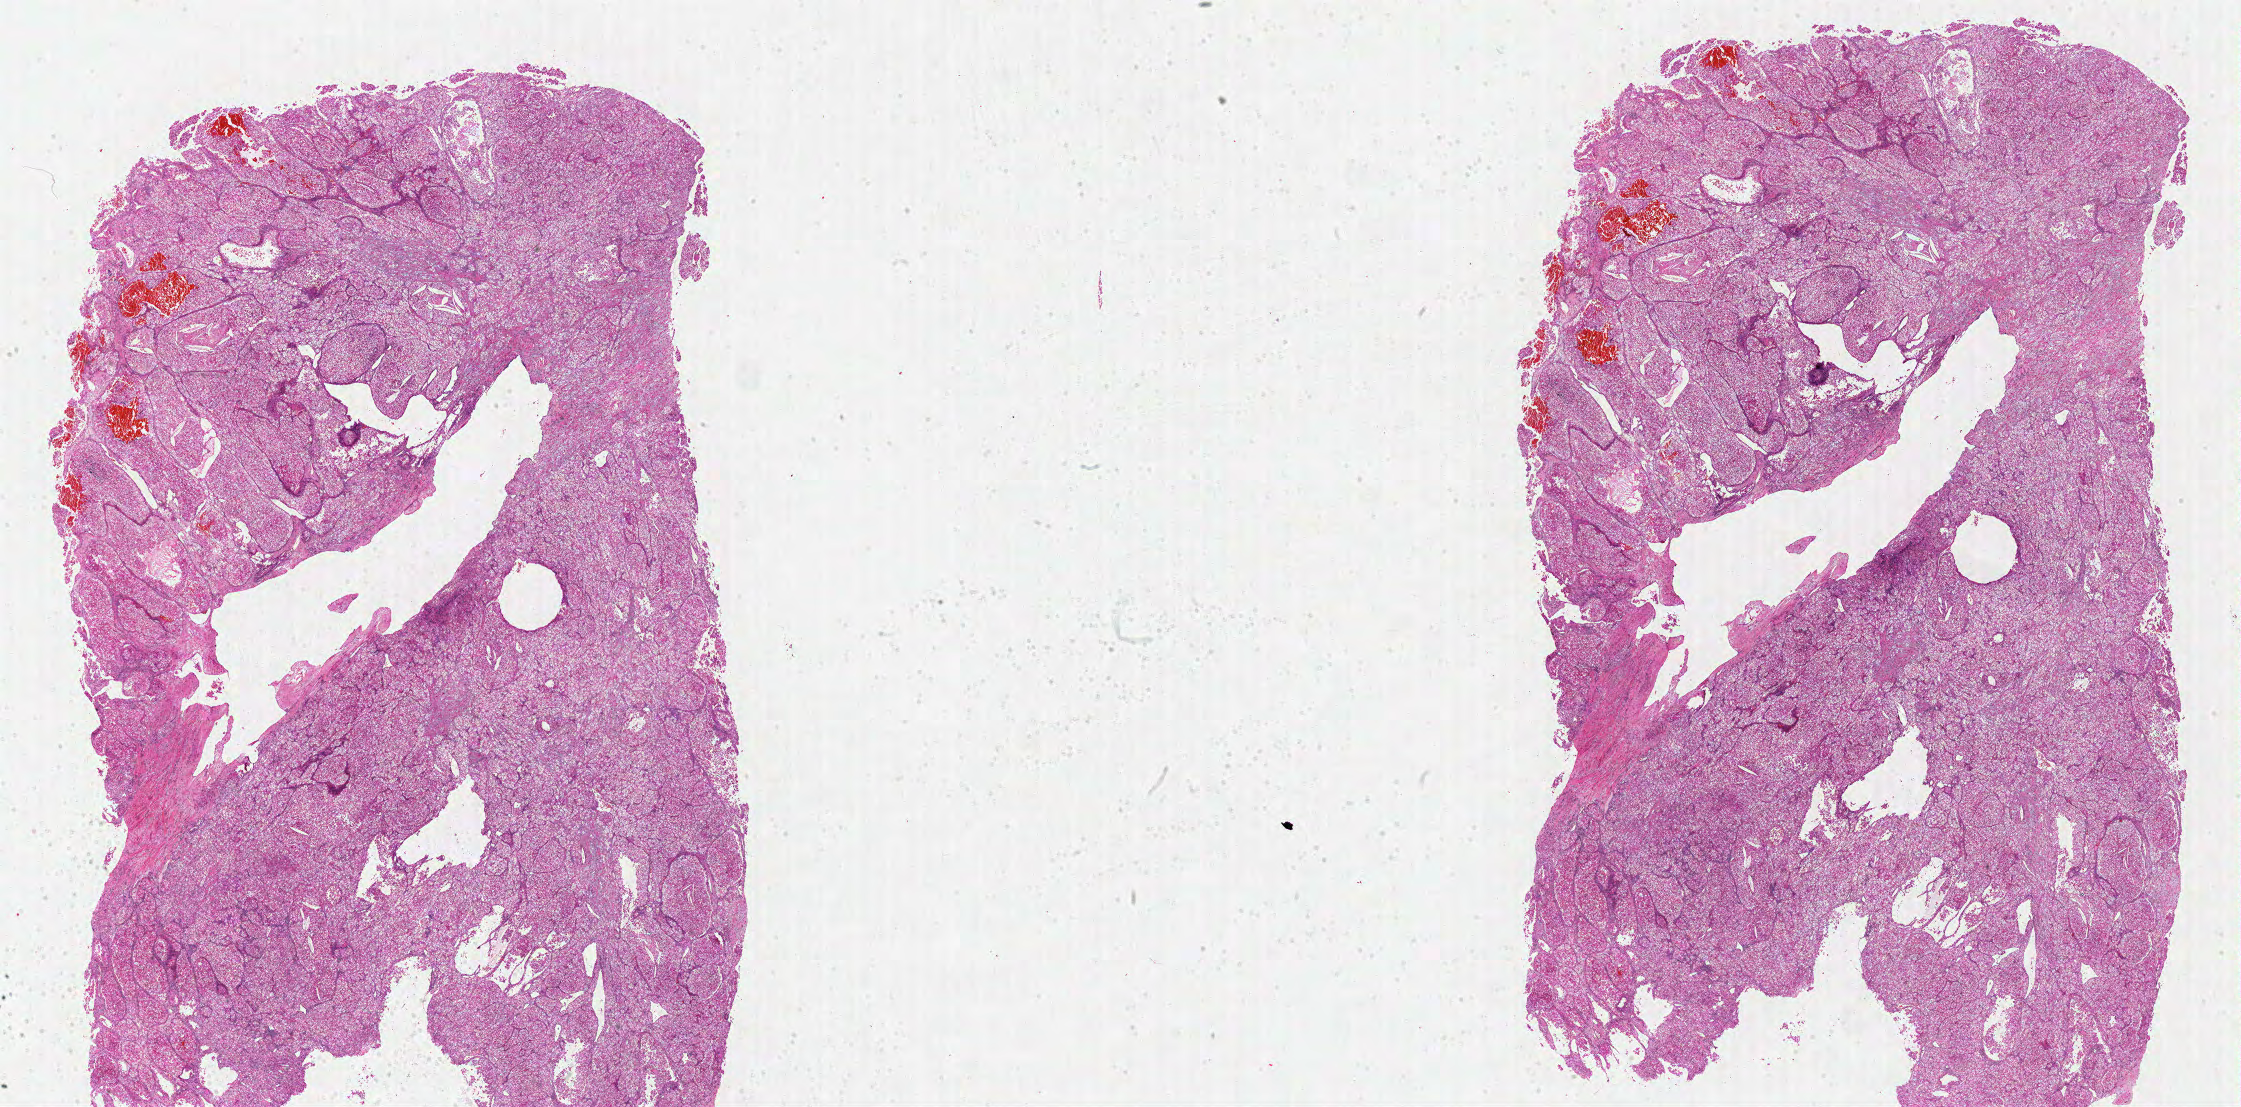
Whole-slide histology image, Hematoxylin and eosin (H&E) stained, a low-resolution overview of the entire scanned area, about 35.2 x 17.4 mm (acquisition: 40x scan). Formalin-fixed paraffin-embedded (FFPE) diagnostic section. Primary tumour sample from the kidney. Male patient; age at initial diagnosis 71 years. Histologic grade: G3 (poorly differentiated).
Diagnosis: Clear cell adenocarcinoma, NOS. Laterality: right. Lymph nodes positive (case pathology): 0 of 3 examined. AJCC pathologic stage: III.